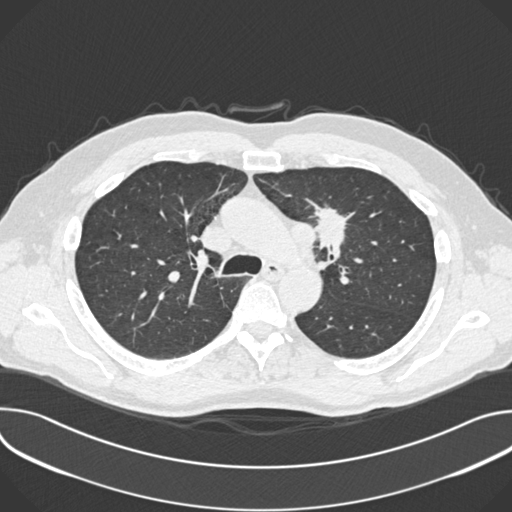
Low-dose screening chest CT, one axial slice; lung window (W 1500 / L -600 HU); 1 mm slice thickness; 512 × 512 image matrix.
Annotated regions visible in this slice (outlined manually by an expert reader):
- lesion 1 (tumor, upper lobe of left lung): bounding box (x1, y1, x2, y2) in pixels: (315, 207, 347, 248)